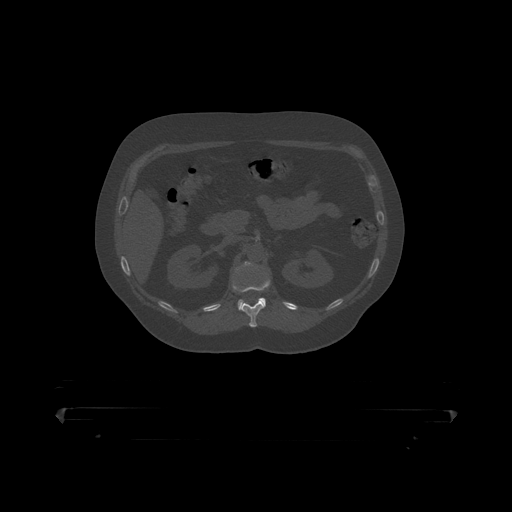
CT including the spine, one axial slice; slice 160 of 390 in the series (ordered by position); reconstruction kernel STANDARD; 120 kVp; bone window (W 1800 / L 400 HU); 1.25 mm slice thickness; 512 × 512 image matrix. Male patient, age 60 years. Case-level facts recorded for this patient, not image findings: primary cancer: prostate.
Annotated regions visible in this slice (semi-automatic segmentation, software-assisted and operator-edited):
- L1 vertebra: bounding box (x1, y1, x2, y2) in pixels: (236, 262, 266, 310)
- T12 vertebra: (233, 272, 271, 319)